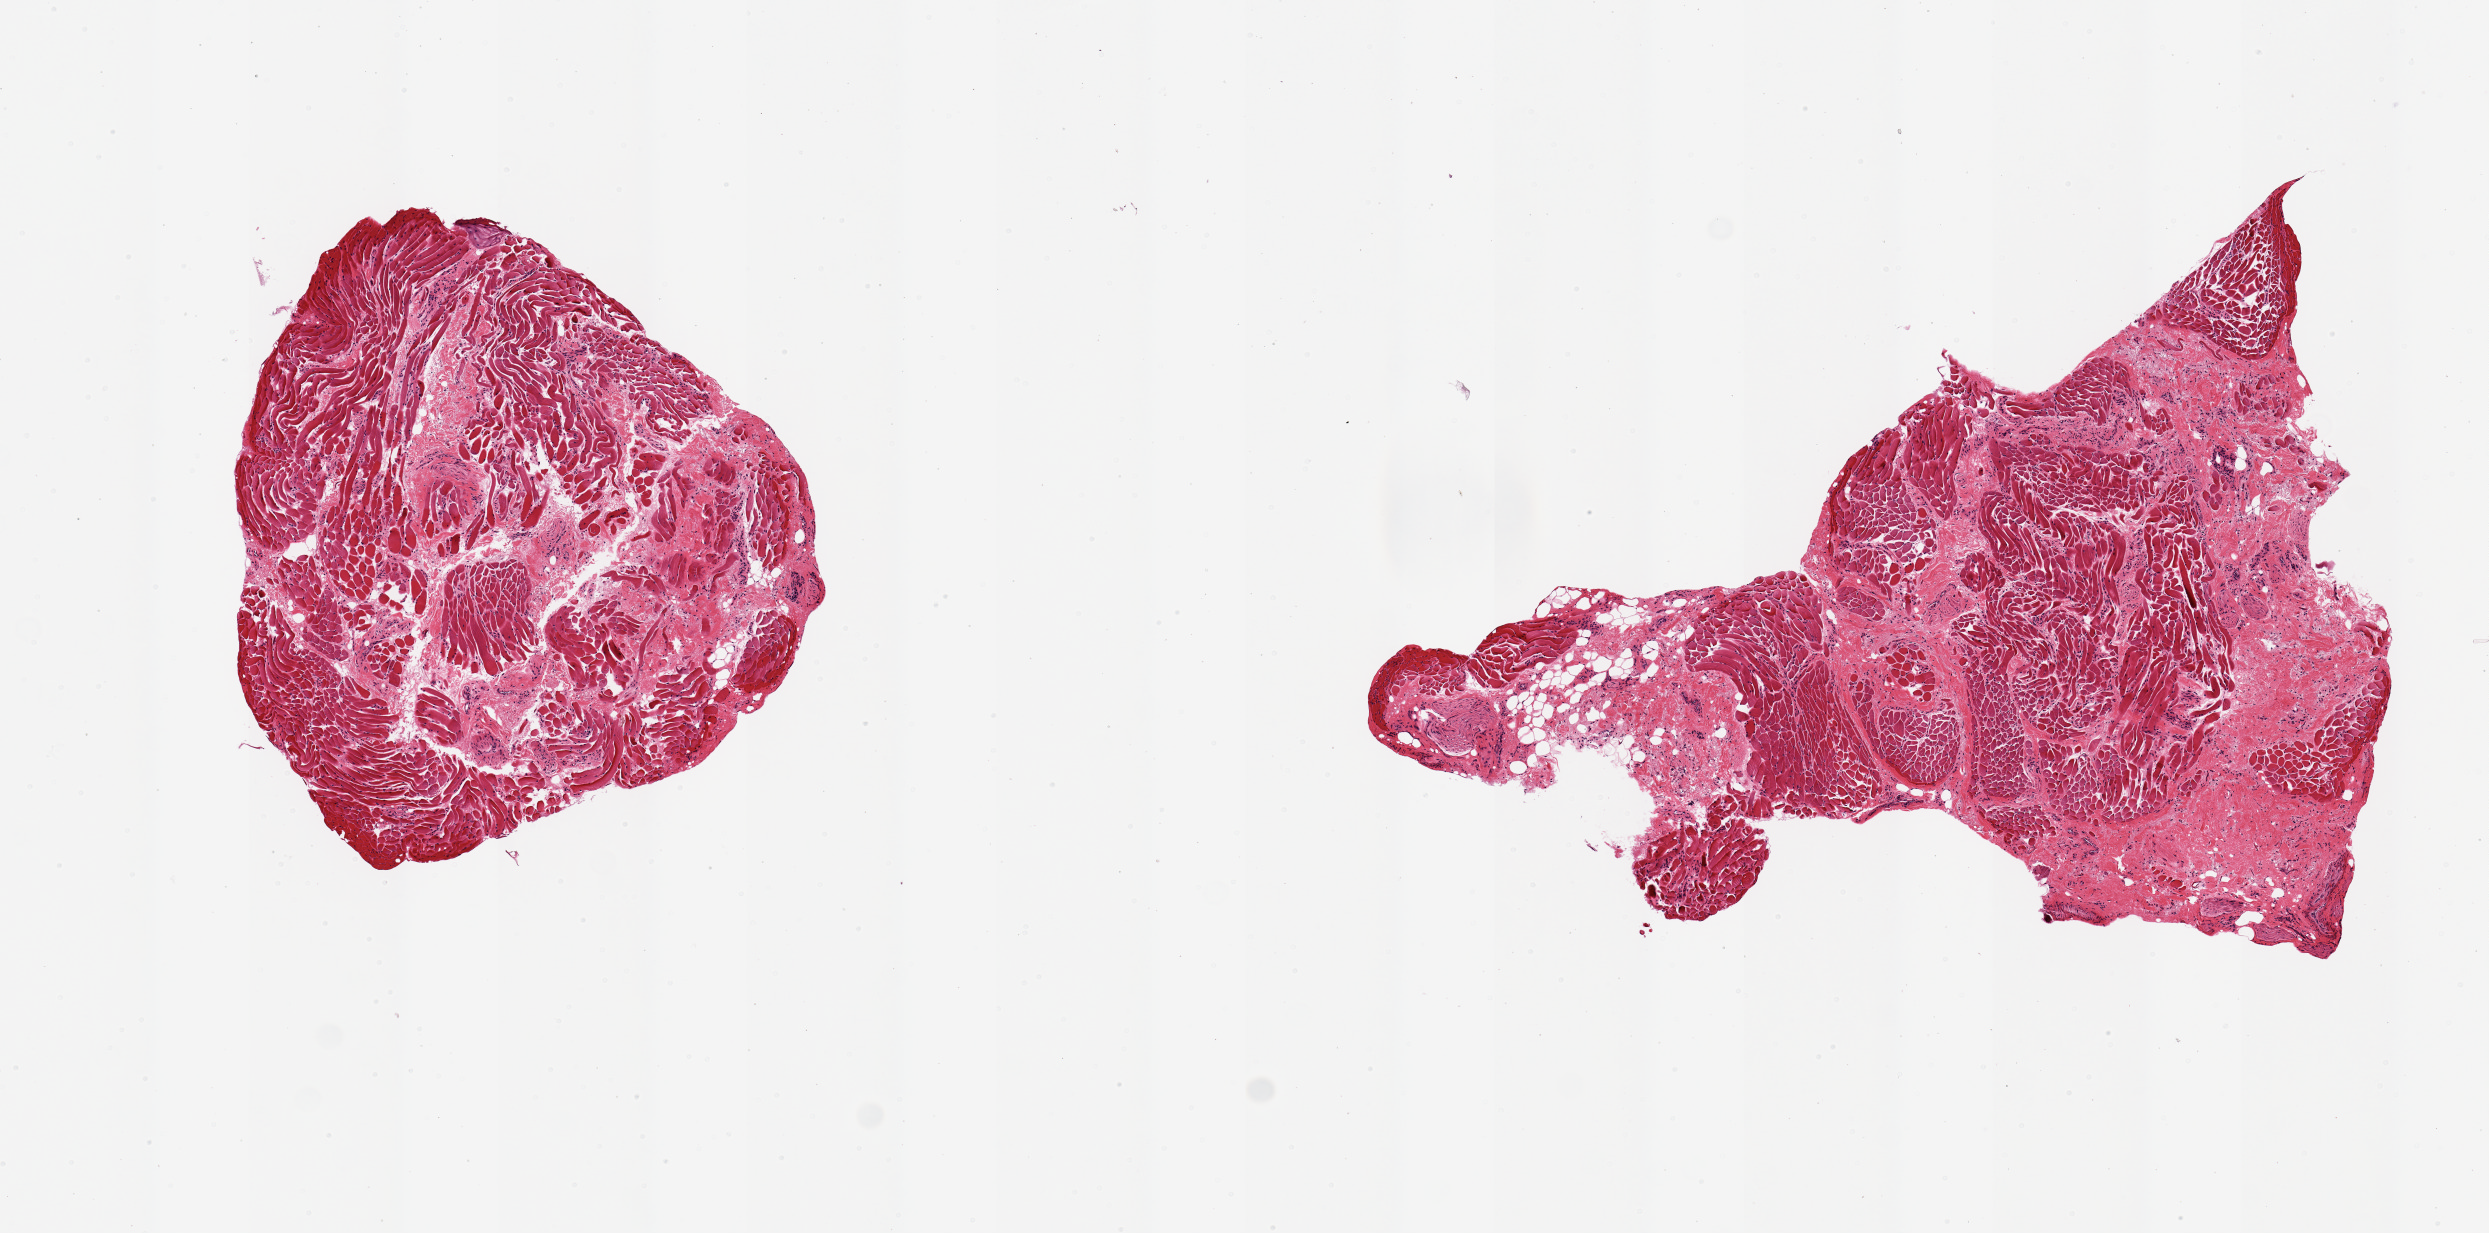
Digitized haematoxylin and eosin-stained section, low-resolution overview of the scanned area, about 9.8 x 4.9 mm; PAXgene-fixed paraffin-embedded (PFPE) section; target tissue: minor salivary gland; tissue donor sample. Female donor.
Reviewer comment on this tissue sample: 2 pieces, muscle, stroma and nerve only.